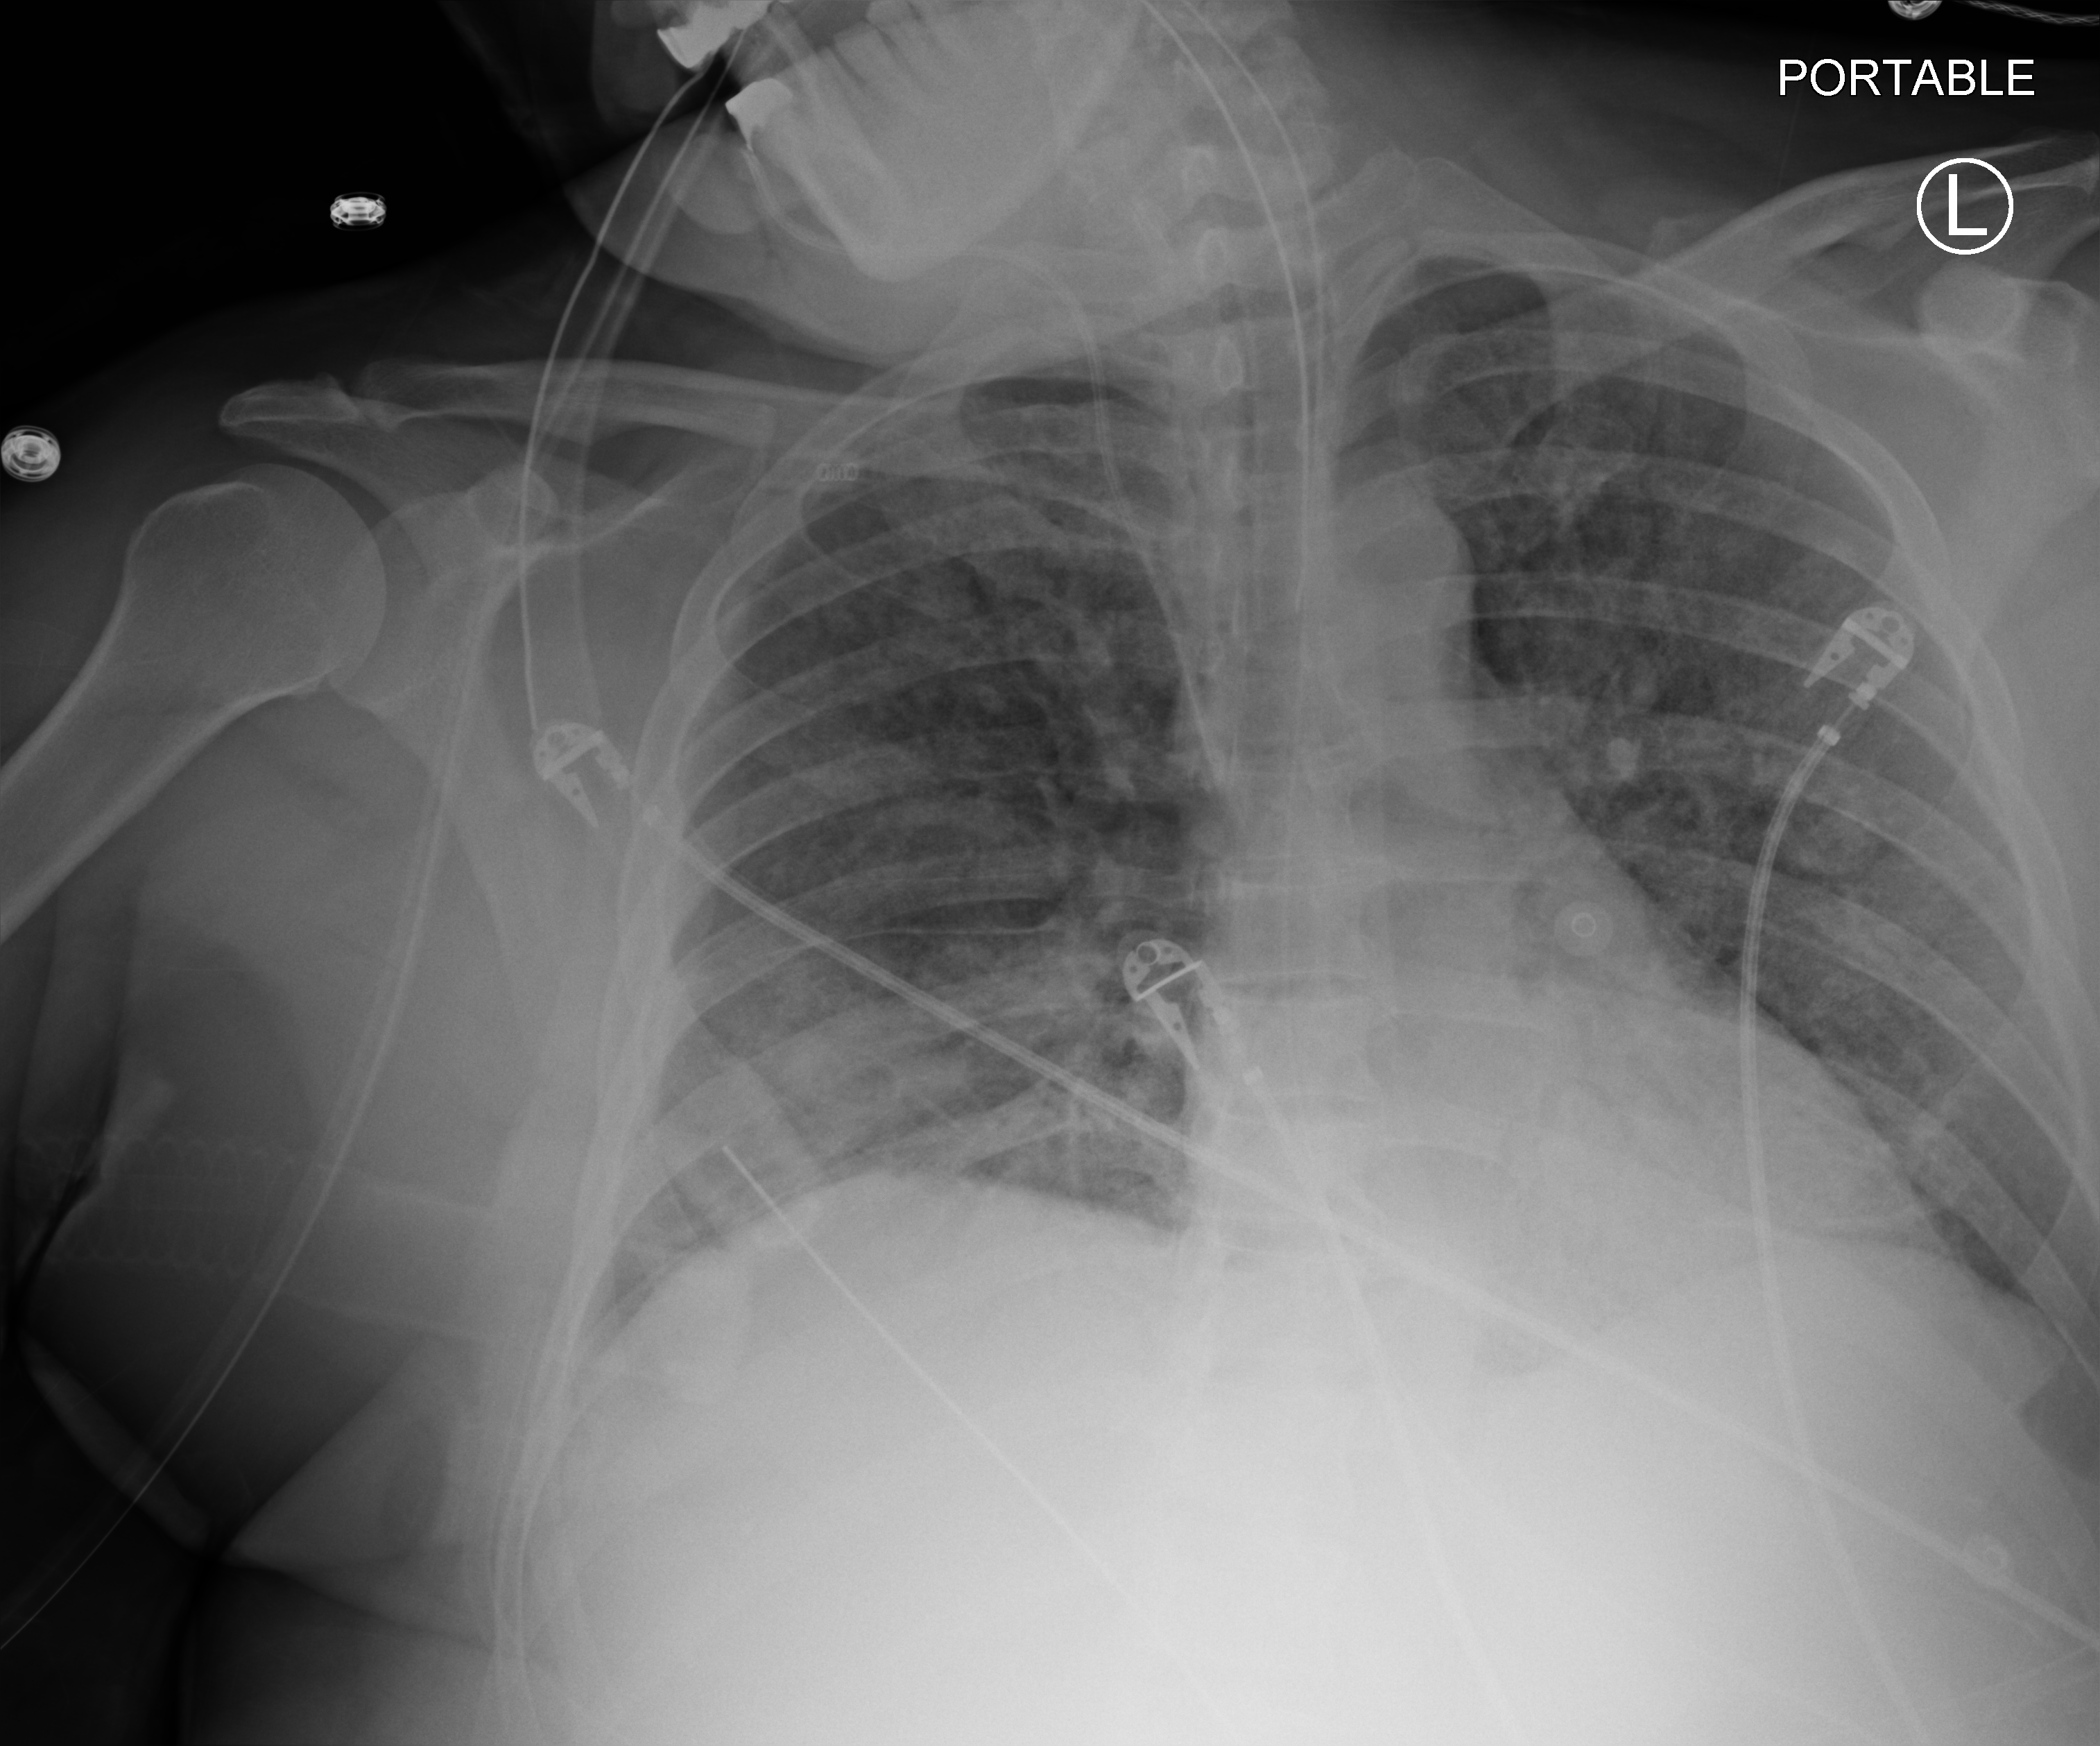
Portable chest radiograph; anteroposterior (AP) projection. Patient hospitalised with COVID-19; male, aged 18–59 years.
Admission-level facts for this patient (not findings on this image; timing relative to this image not recorded): smoking status (admission record): never; mechanically ventilated during this hospital stay: yes.